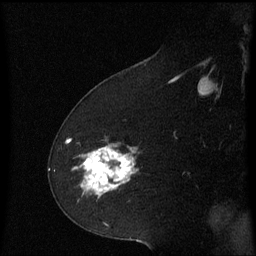
Breast MRI (dynamic contrast-enhanced), one sagittal slice; dynamic contrast-enhanced series, image 2 of 3 at this slice position (ordered by acquisition); 1.5 T; TE 4.2 ms, TR 8.4 ms; 256 × 256 image matrix, field of view 200 × 200 mm. Female patient, age 60 years. From the clinical record (not read from this slice): setting: breast cancer imaged before/during neoadjuvant chemotherapy; receptor status: triple-negative.
Annotated regions visible in this slice (semi-automatic segmentation, software-assisted and operator-edited):
- analysis volume of interest (the breast-tissue region the enhancement analysis was run in; not a lesion): box from (x=72, y=142) to (x=140, y=203) px
- tumour enhancement mask (voxels above the 70 % enhancement threshold inside the analysis volume of interest): (x=76, y=146)–(x=135, y=193)